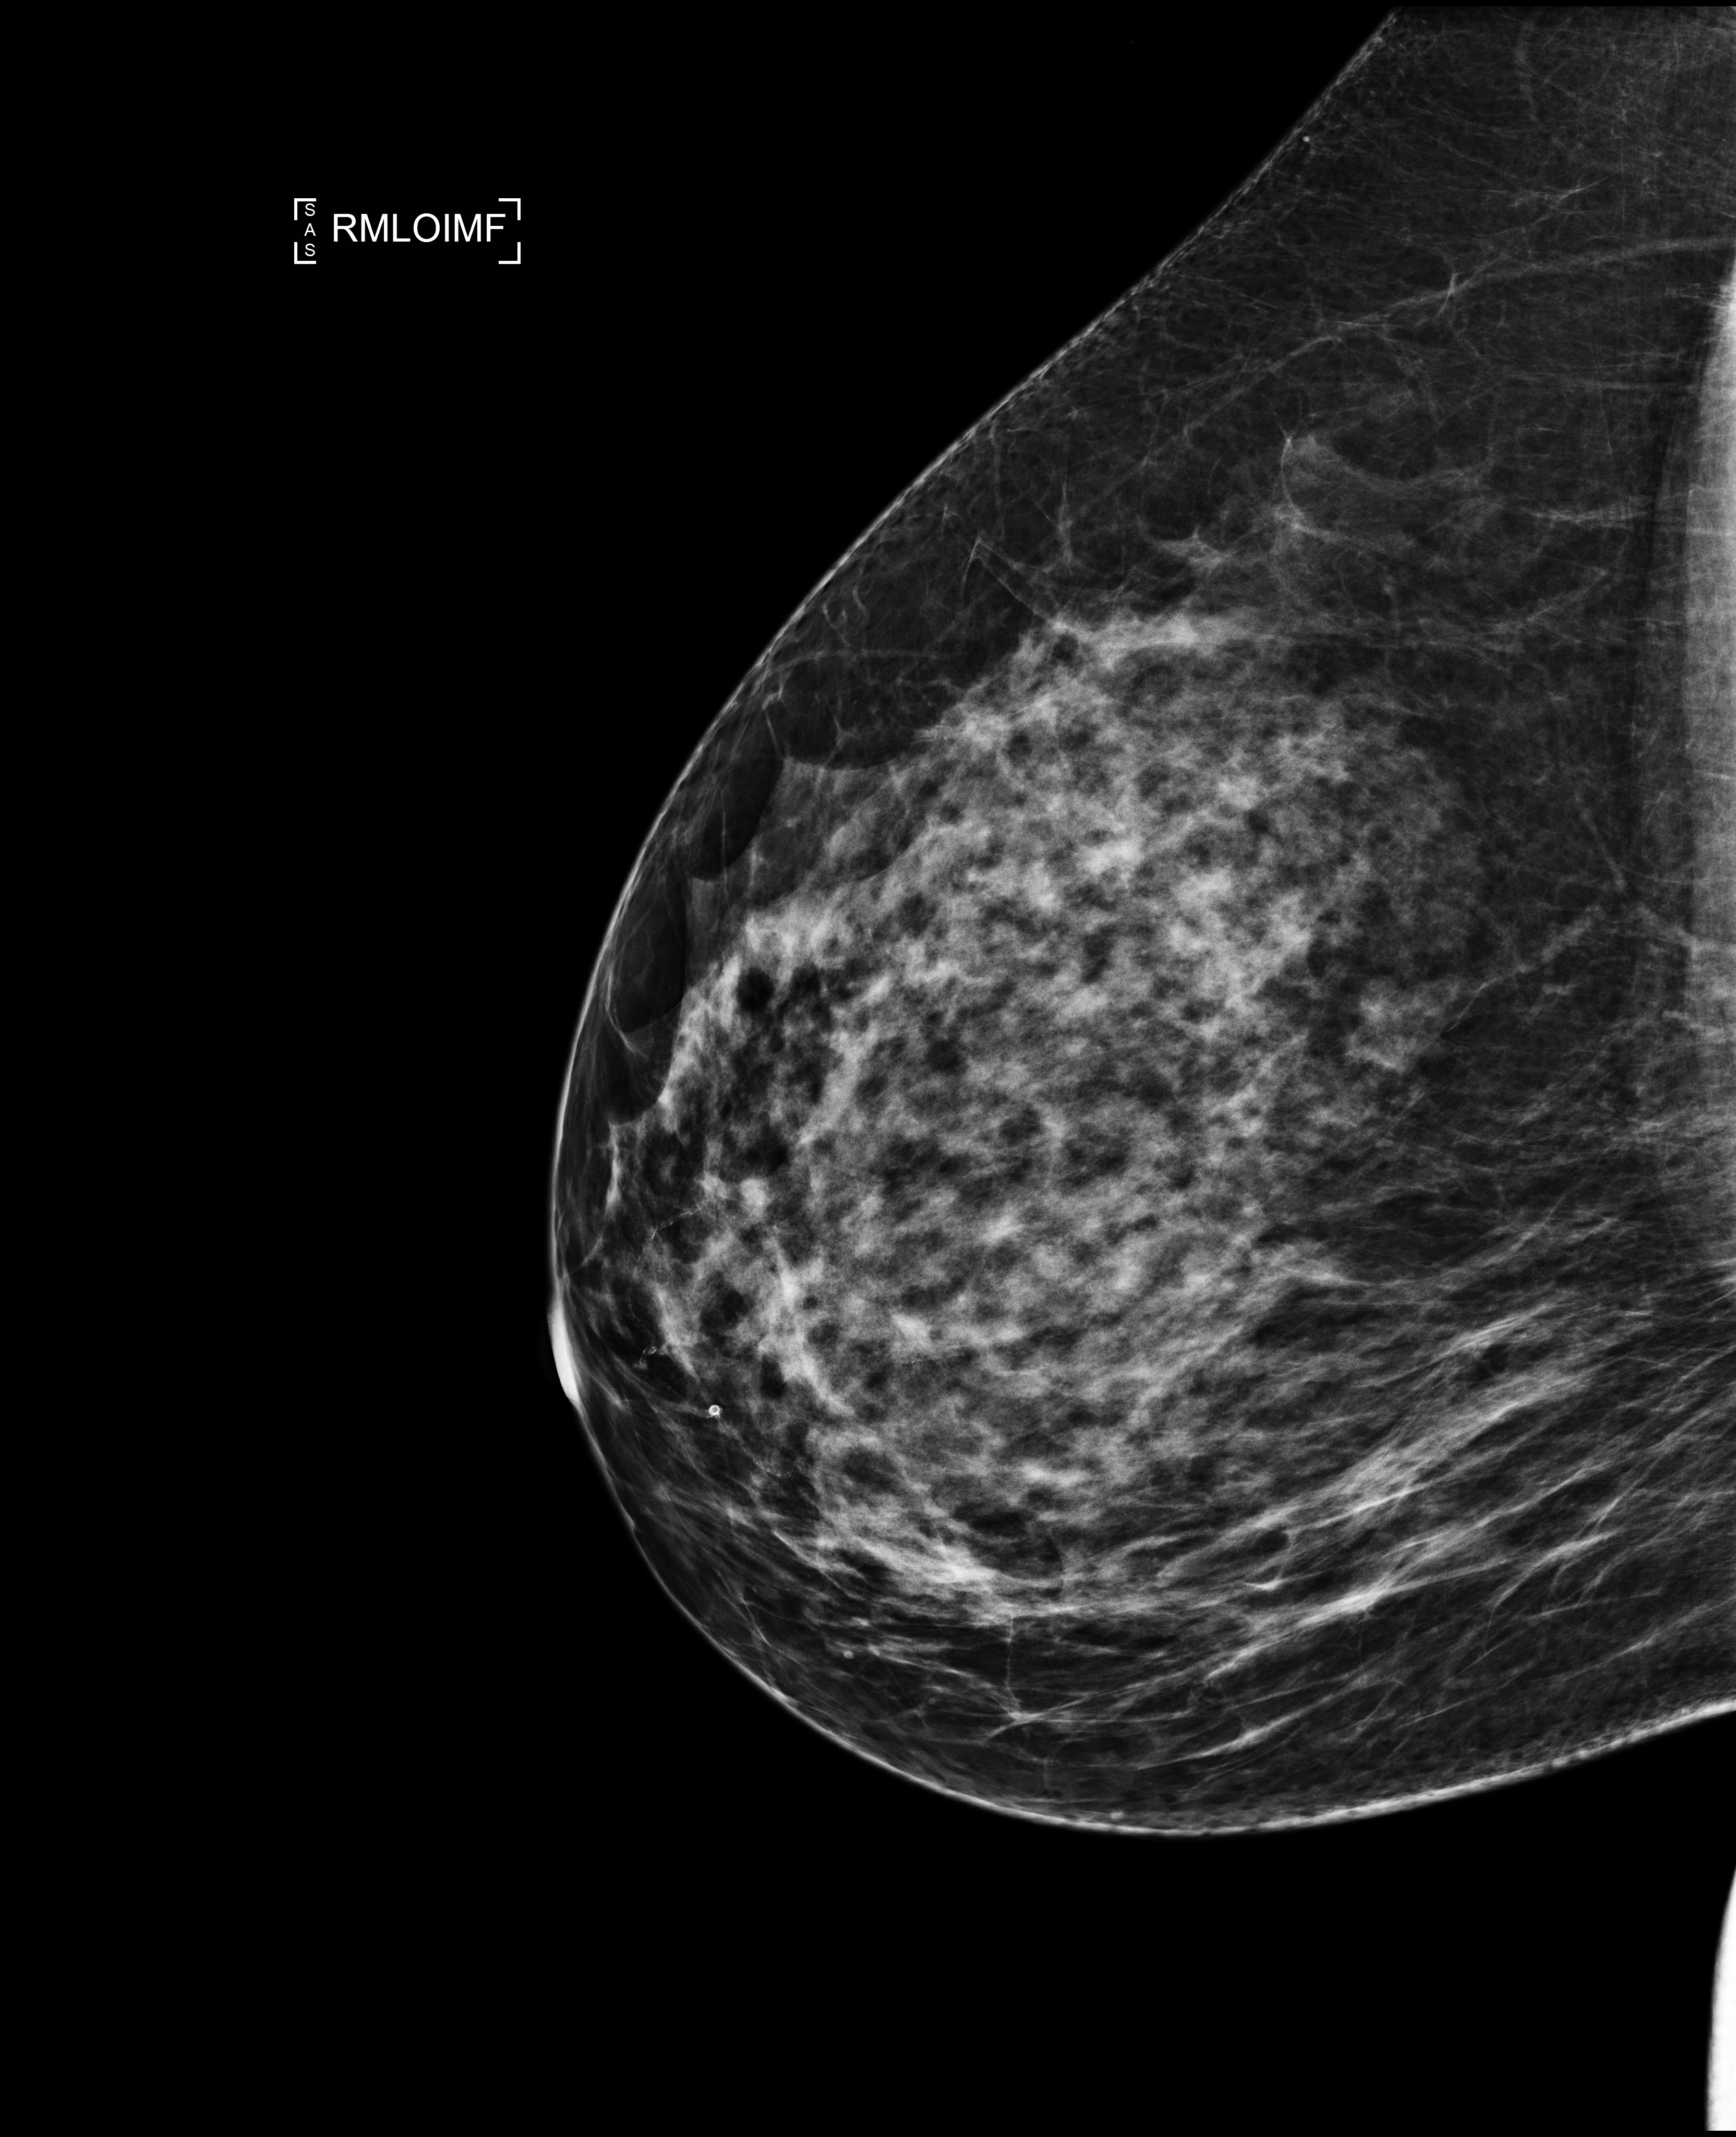
Full-field digital mammogram (FFDM); right breast; medio-lateral oblique projection (infra-mammary fold); screening examination. Patient: female, 44 years.
Breast density at the screening exam (both breasts): heterogeneously dense (BI-RADS density category c). Final BI-RADS assessment for this screening round (tomosynthesis exam, both breasts): category 1. Recall: no recall after this screen.